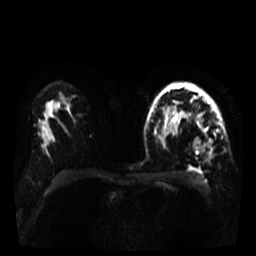
Breast MRI, one axial slice; diffusion-weighted series; image 2 of 4 stored at this slice position (different b-values; order by instance number); 3 T; 5 mm slice thickness; 256 × 256 image matrix, field of view 320 × 320 mm. Female patient.
Outlined on this slice (manually delineated by an expert):
- tumour on diffusion-weighted imaging: bounding box [x1, y1, x2, y2] px = [194, 138, 212, 155]